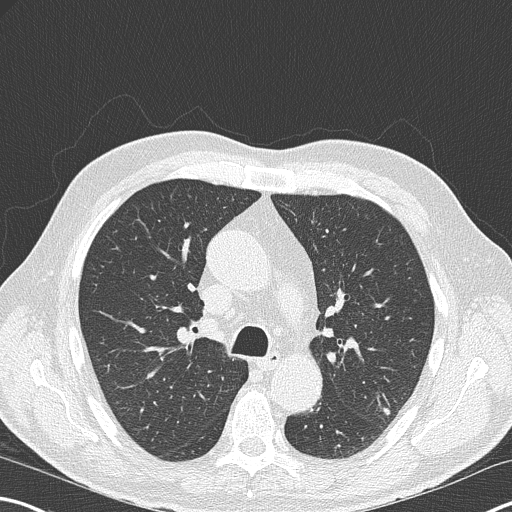
Low-dose screening chest CT, axial slice, second screening round (one year after baseline), lung window (W 1500 / L -600 HU), 2 mm slice thickness. Male, age 67 years at enrolment. Former smoker at enrolment.
Expert reader's lesion annotation, bounding box [x1, y1, x2, y2] px = [371, 391, 411, 430]. Screening reader's record for this exam (one nodule recorded; not confirmed to be the boxed lesion): non-calcified nodule or mass ≥4 mm, left upper lobe, 9 × 6 mm, poorly defined margins, soft tissue attenuation, pre-existing on the prior screen: no. Later outcome: lung cancer diagnosed 418 days after this screen (after the third annual screen) — squamous cell carcinoma, large cell, nonkeratinizing, NOS, left upper lobe, moderately differentiated (G2), stage IA (AJCC 6th edition), 15 mm at pathology.